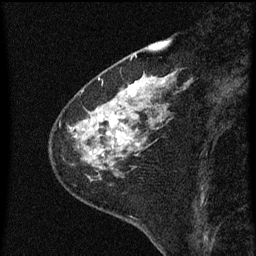
Breast MRI (dynamic contrast-enhanced), one sagittal slice; position 17 of 60 along the scan axis; dynamic contrast-enhanced series, image 2 of 3 at this slice position (ordered by acquisition); 1.5 T; TE 4.2 ms, TR 8 ms; 2 mm slice thickness; 256 × 256 image matrix. Patient: female, 60 years.
Outlined on this slice (semi-automatically segmented with operator editing):
- analysis volume of interest (the breast-tissue region the enhancement analysis was run in; not a lesion): box from (x=52, y=82) to (x=159, y=181) px
- tumour enhancement mask (voxels above the 70 % enhancement threshold inside the analysis volume of interest): (x=90, y=82)–(x=141, y=155)